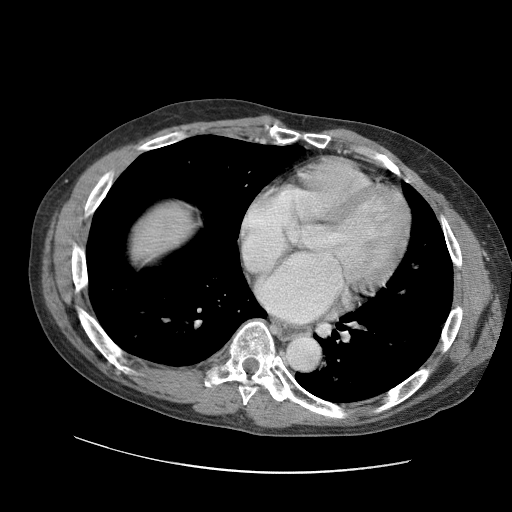
Contrast-enhanced abdominal CT (liver protocol), one axial slice. Position 99 of 109 along the scan axis. 120 kVp. Soft-tissue window (W 400 / L 40 HU). 2.5 mm slice thickness. 512 × 512 image matrix, field of view 400 × 400 mm. From the clinical record (not read from this slice): diagnosis: hepatocellular carcinoma (patient treated with transarterial chemoembolisation; whether this scan precedes or follows treatment is not stated here); TNM stage (as recorded): Stage-IIIC; Child-Pugh class: B.
Outlined on this slice (semi-automatic segmentation, software-assisted and operator-edited):
- liver parenchyma outside the tumour (the mass and vessels are separate outlines, so this box may not span the whole liver): box from (x=132, y=206) to (x=192, y=258) px
- liver vessels: (x=181, y=216)–(x=184, y=219)